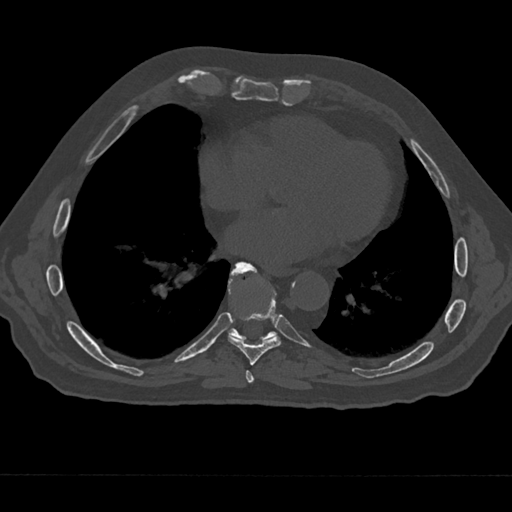
CT including the spine, one axial slice; position 299 of 797 along the scan axis; reconstruction kernel Br40s/3; 120 kVp; bone window (W 1800 / L 400 HU); 0.5 mm slice thickness; 512 × 512 image matrix, field of view 377 × 377 mm. Male patient, age 75 years. From the clinical record (not read from this slice): primary cancer: renal.
Structures marked on this image (semi-automatic segmentation, software-assisted and operator-edited):
- T7 vertebra: box from (x=242, y=369) to (x=258, y=385) px
- T8 vertebra: (x=228, y=267)–(x=281, y=365)
- T9 vertebra: (x=228, y=261)–(x=277, y=341)